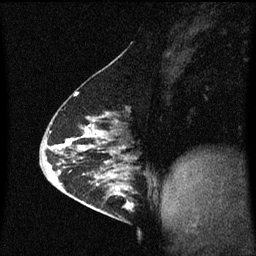
Breast MRI (dynamic contrast-enhanced), one sagittal slice; slice 31 of 60 in the series (ordered by position); dynamic contrast-enhanced series, image 2 of 3 at this slice position (ordered by acquisition); 1.5 T; TE 4.2 ms, TR 8.4 ms; 2 mm slice thickness; 256 × 256 image matrix, field of view 200 × 200 mm. Female patient, age 63 years.
Outlined on this slice (semi-automatic segmentation, software-assisted and operator-edited):
- analysis volume of interest (the breast-tissue region the enhancement analysis was run in; not a lesion): bounding box [x1, y1, x2, y2] px = [98, 168, 137, 217]
- tumour enhancement mask (voxels above the 70 % enhancement threshold inside the analysis volume of interest): [98, 170, 135, 209]